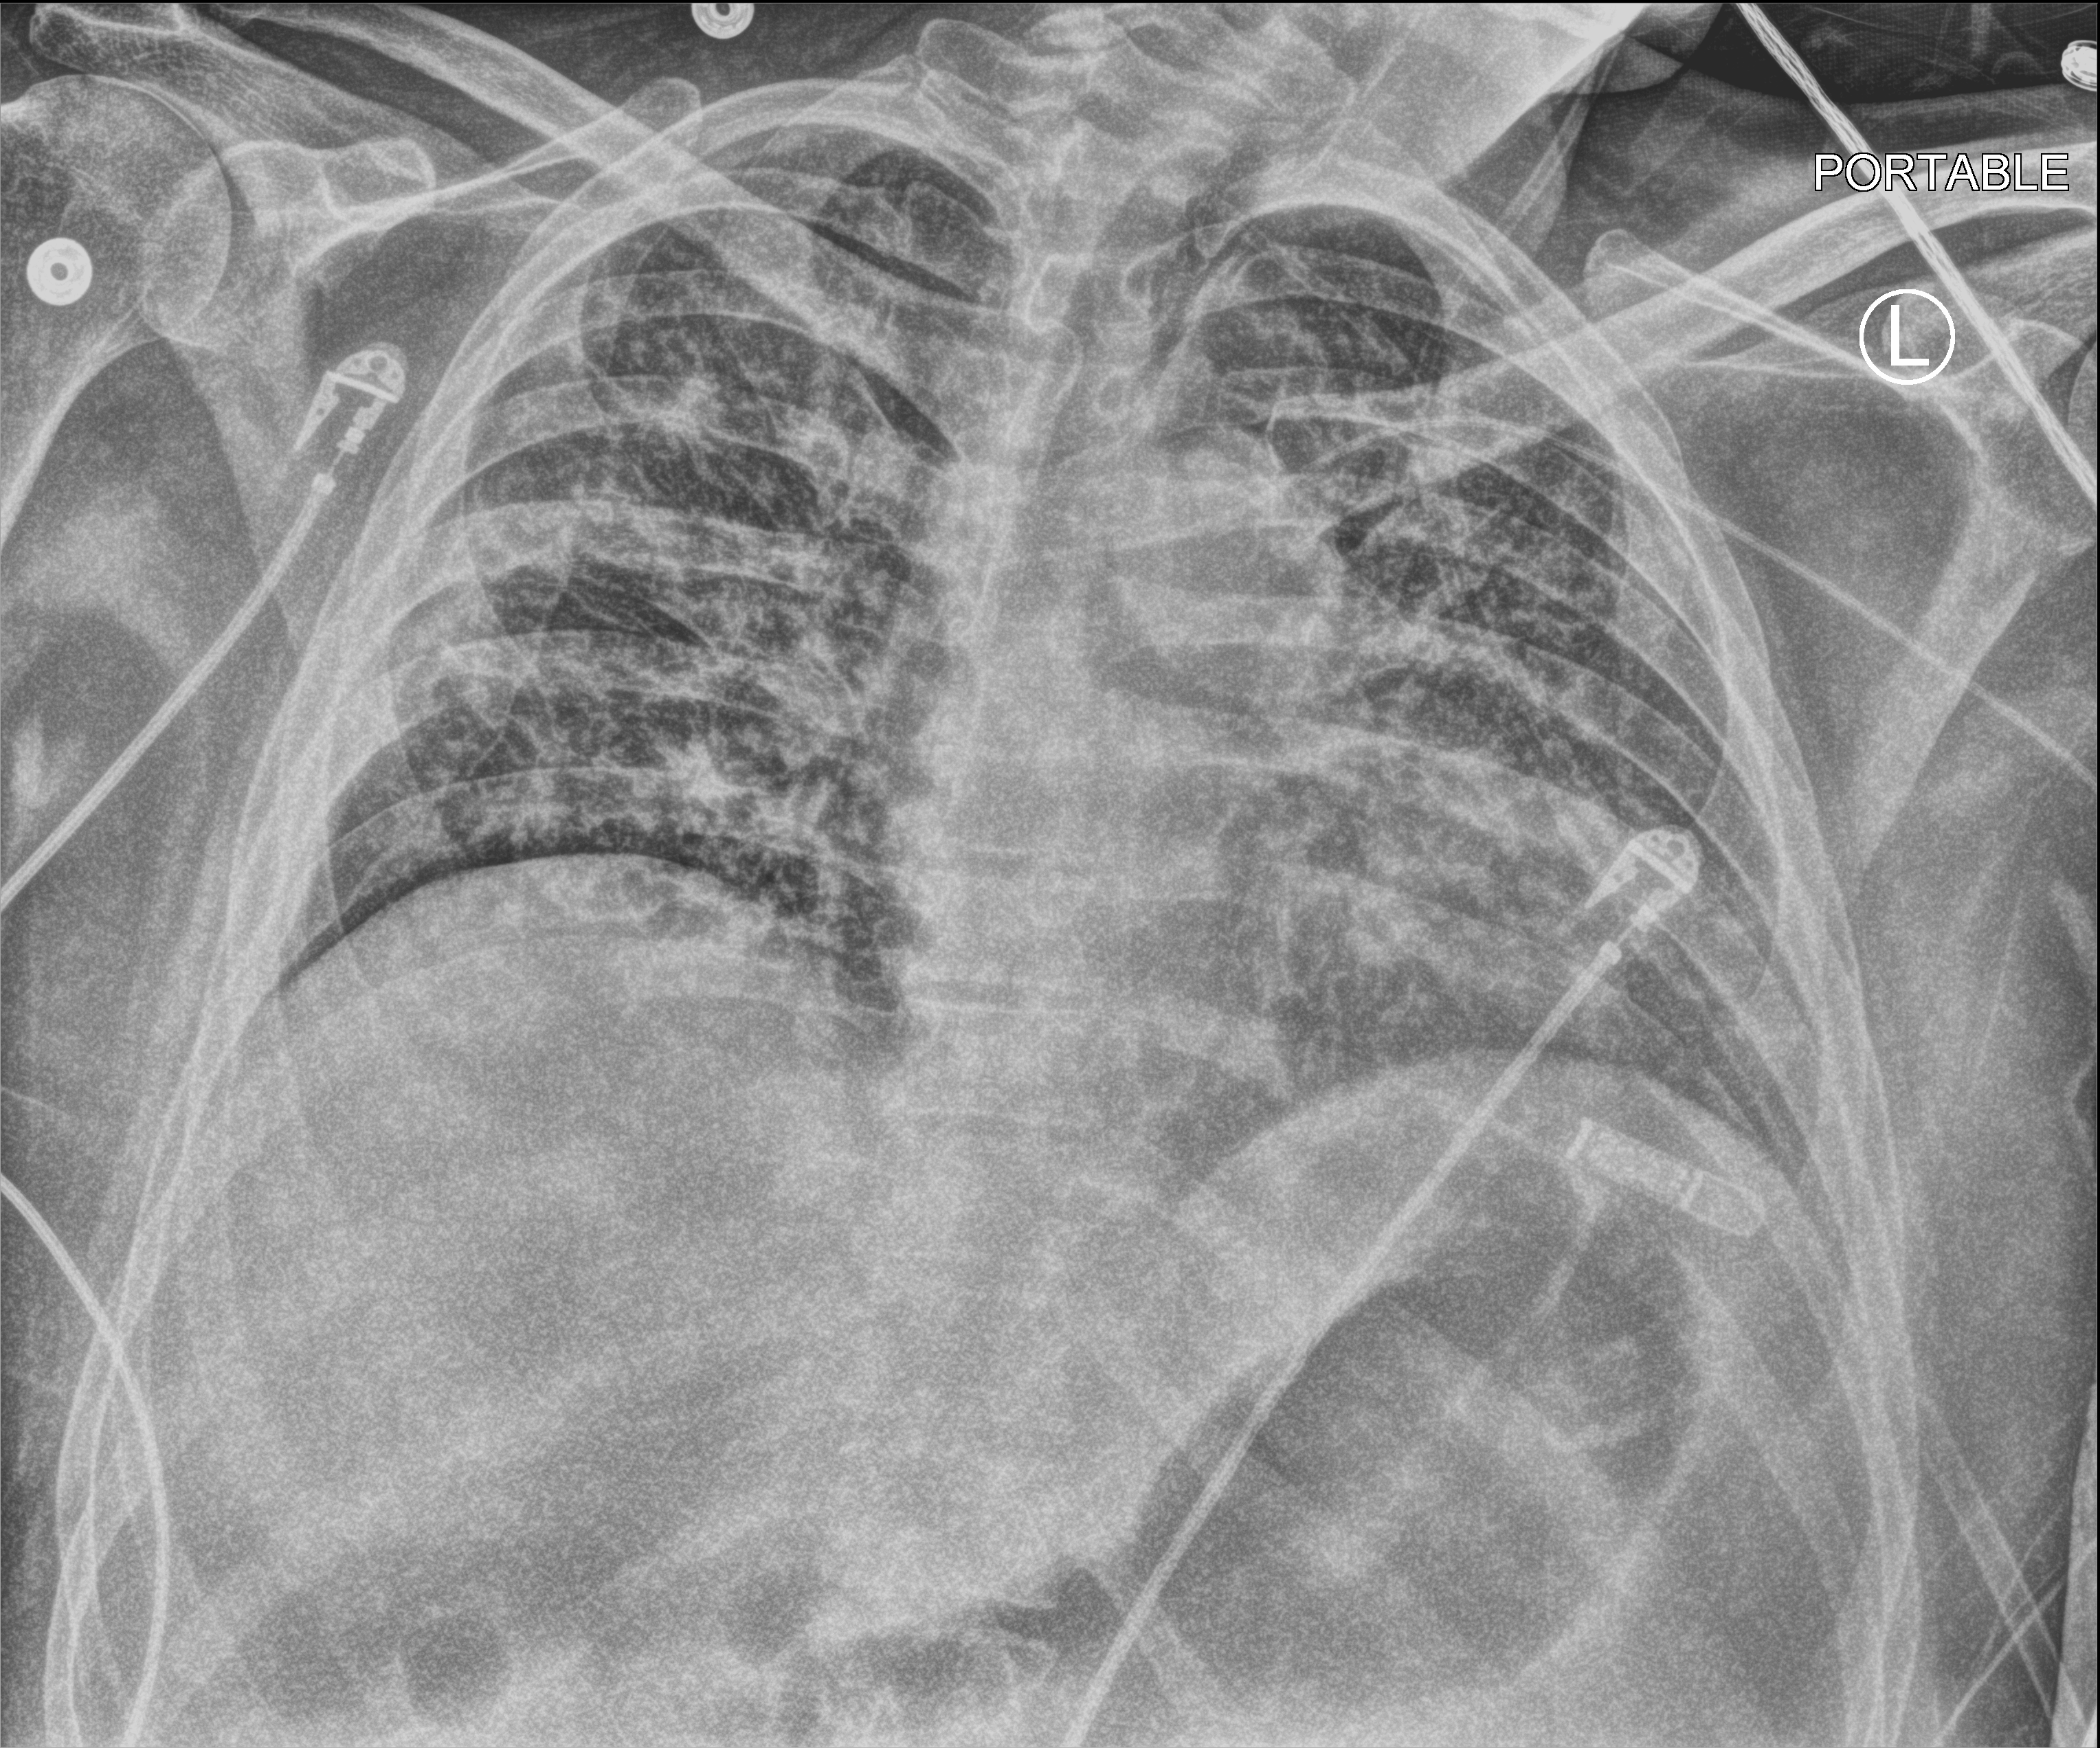
Portable chest radiograph. Patient hospitalised with COVID-19; male, aged 18–59 years.
Hospital-stay facts (about this admission, not read from this image; timing relative to this image not recorded): mechanically ventilated during this hospital stay: yes; admitted to intensive care during this hospital stay: yes.